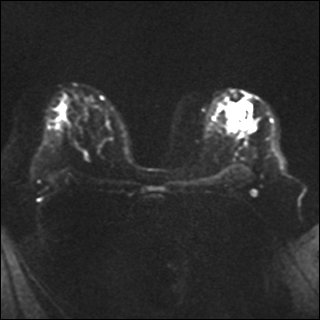
Breast MRI, one axial slice; position 21 of 35 along the scan axis; diffusion-weighted series; image 2 of 4 stored at this slice position (different b-values; order by instance number); 1.5 T; 4 mm slice thickness; 320 × 320 image matrix, field of view 320 × 320 mm. Female patient.
Structures marked on this image (manually delineated by an expert):
- tumour on diffusion-weighted imaging: box from (x=232, y=122) to (x=237, y=126) px